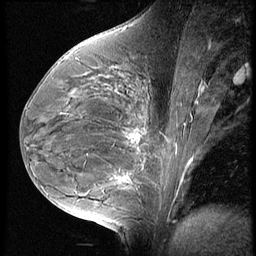
Breast MRI (dynamic contrast-enhanced), one sagittal slice. 3 images stored at this slice position (order not interpretable as contrast timing). 1.5 T. TE 4.2 ms, TR 9 ms. 256 × 256 image matrix, field of view 180 × 180 mm. Female patient, age 35 years. Case-level facts recorded for this patient, not image findings: setting: breast cancer imaged before/during neoadjuvant chemotherapy; receptor status: HR-positive, HER2-negative.
Structures marked on this image (semi-automatic segmentation, software-assisted and operator-edited):
- analysis volume of interest (the breast-tissue region the enhancement analysis was run in; not a lesion): box from (x=56, y=58) to (x=176, y=202) px
- tumour enhancement mask (voxels above the 140 % enhancement threshold inside the analysis volume of interest): (x=114, y=135)–(x=137, y=181)